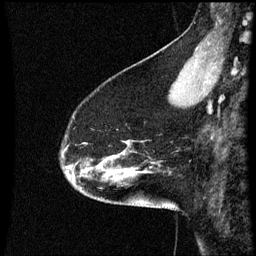
Breast MRI (dynamic contrast-enhanced), one sagittal slice; slice 13 of 60 in the series (ordered by position); dynamic contrast-enhanced series, image 2 of 3 at this slice position (ordered by acquisition); 1.5 T; TE 4.2 ms, TR 8.9 ms; 2 mm slice thickness; 256 × 256 image matrix, field of view 200 × 200 mm. Patient: female, 45 years. From the clinical record (not read from this slice): setting: breast cancer imaged before/during neoadjuvant chemotherapy; receptor status: HR-positive, HER2-negative.
Annotated regions visible in this slice (semi-automatic segmentation, software-assisted and operator-edited):
- analysis volume of interest (the breast-tissue region the enhancement analysis was run in; not a lesion): bounding box <62,94,171,205> (left, top, right, bottom; pixels)
- tumour enhancement mask (voxels above the 70 % enhancement threshold inside the analysis volume of interest): <88,156,117,169>